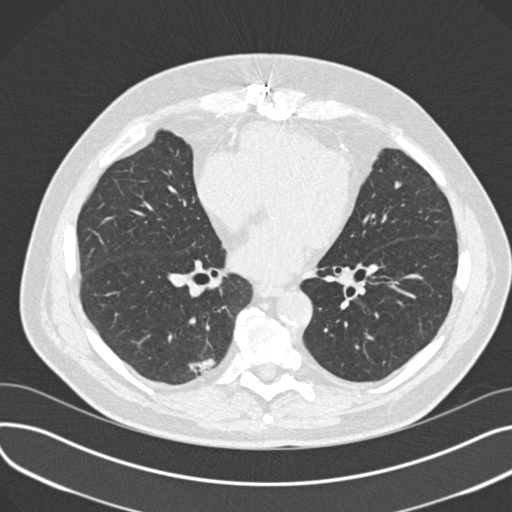
Low-dose screening chest CT, one axial slice; slice 78 of 177 in the series (ordered by position); lung window (W 1500 / L -600 HU); 512 × 512 image matrix, field of view 372 × 372 mm.
Outlined on this slice (manually delineated by an expert):
- lesion 1 (tumor, lower lobe of right lung): bounding box (x1, y1, x2, y2) in pixels: (189, 358, 216, 376)